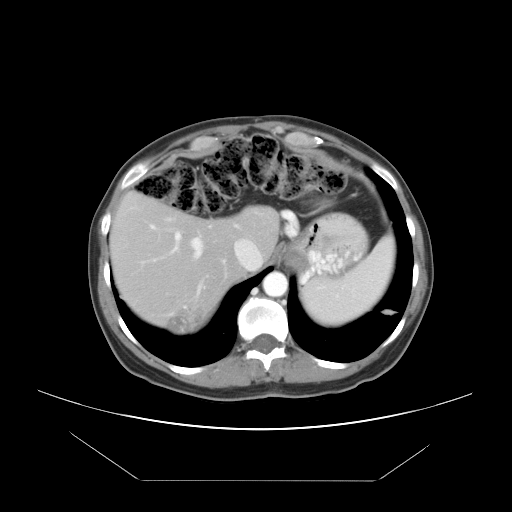
Contrast-enhanced abdominal CT, one axial slice; position 35 of 45 along the scan axis; reconstruction kernel STANDARD; 120 kVp; soft-tissue window (W 400 / L 40 HU); 5 mm slice thickness; 512 × 512 image matrix. Female patient, age 52 years. From the clinical record (not read from this slice): diagnosis: colorectal cancer liver metastases, imaged before liver resection; multiple liver metastases: yes; largest metastasis: 2.5 cm; disease in both lobes: no.
Structures marked on this image (expert manual segmentation):
- hepatic veins: bounding box <164,217,205,297> (left, top, right, bottom; pixels)
- liver: <113,195,278,332>
- planned liver remnant (the part of the liver to remain after resection): <113,195,278,307>
- portal vein (with intrahepatic branches): <150,225,225,262>
- liver metastasis: <169,309,203,332>